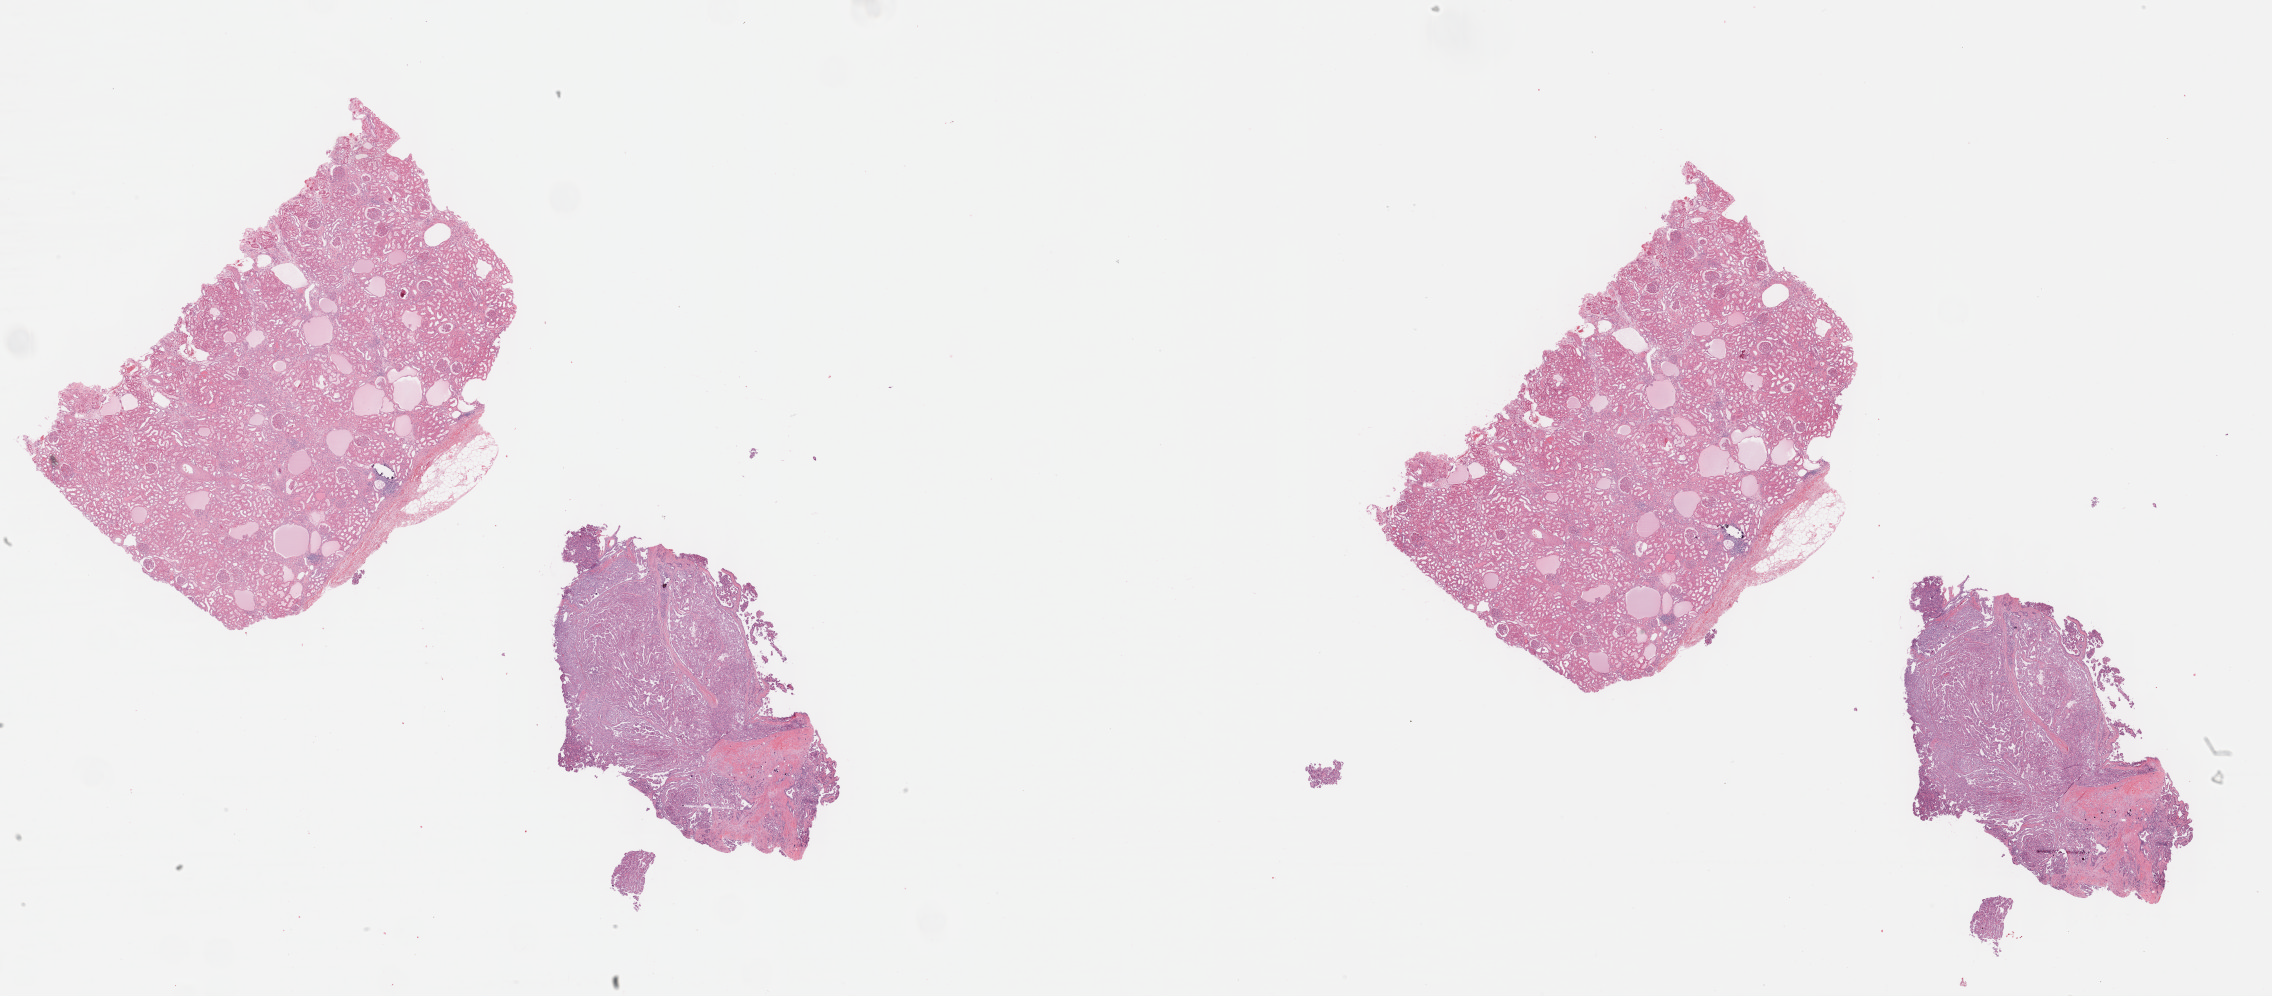
H&E-stained whole-slide image, low-resolution overview of the scanned area, about 36.7 x 16.1 mm, FFPE section, primary tumour sample from the kidney. Male, age 74 years at initial diagnosis.
AJCC pathologic stage: I (7th edition). Laterality: left. Diagnosis: Papillary adenocarcinoma, NOS.